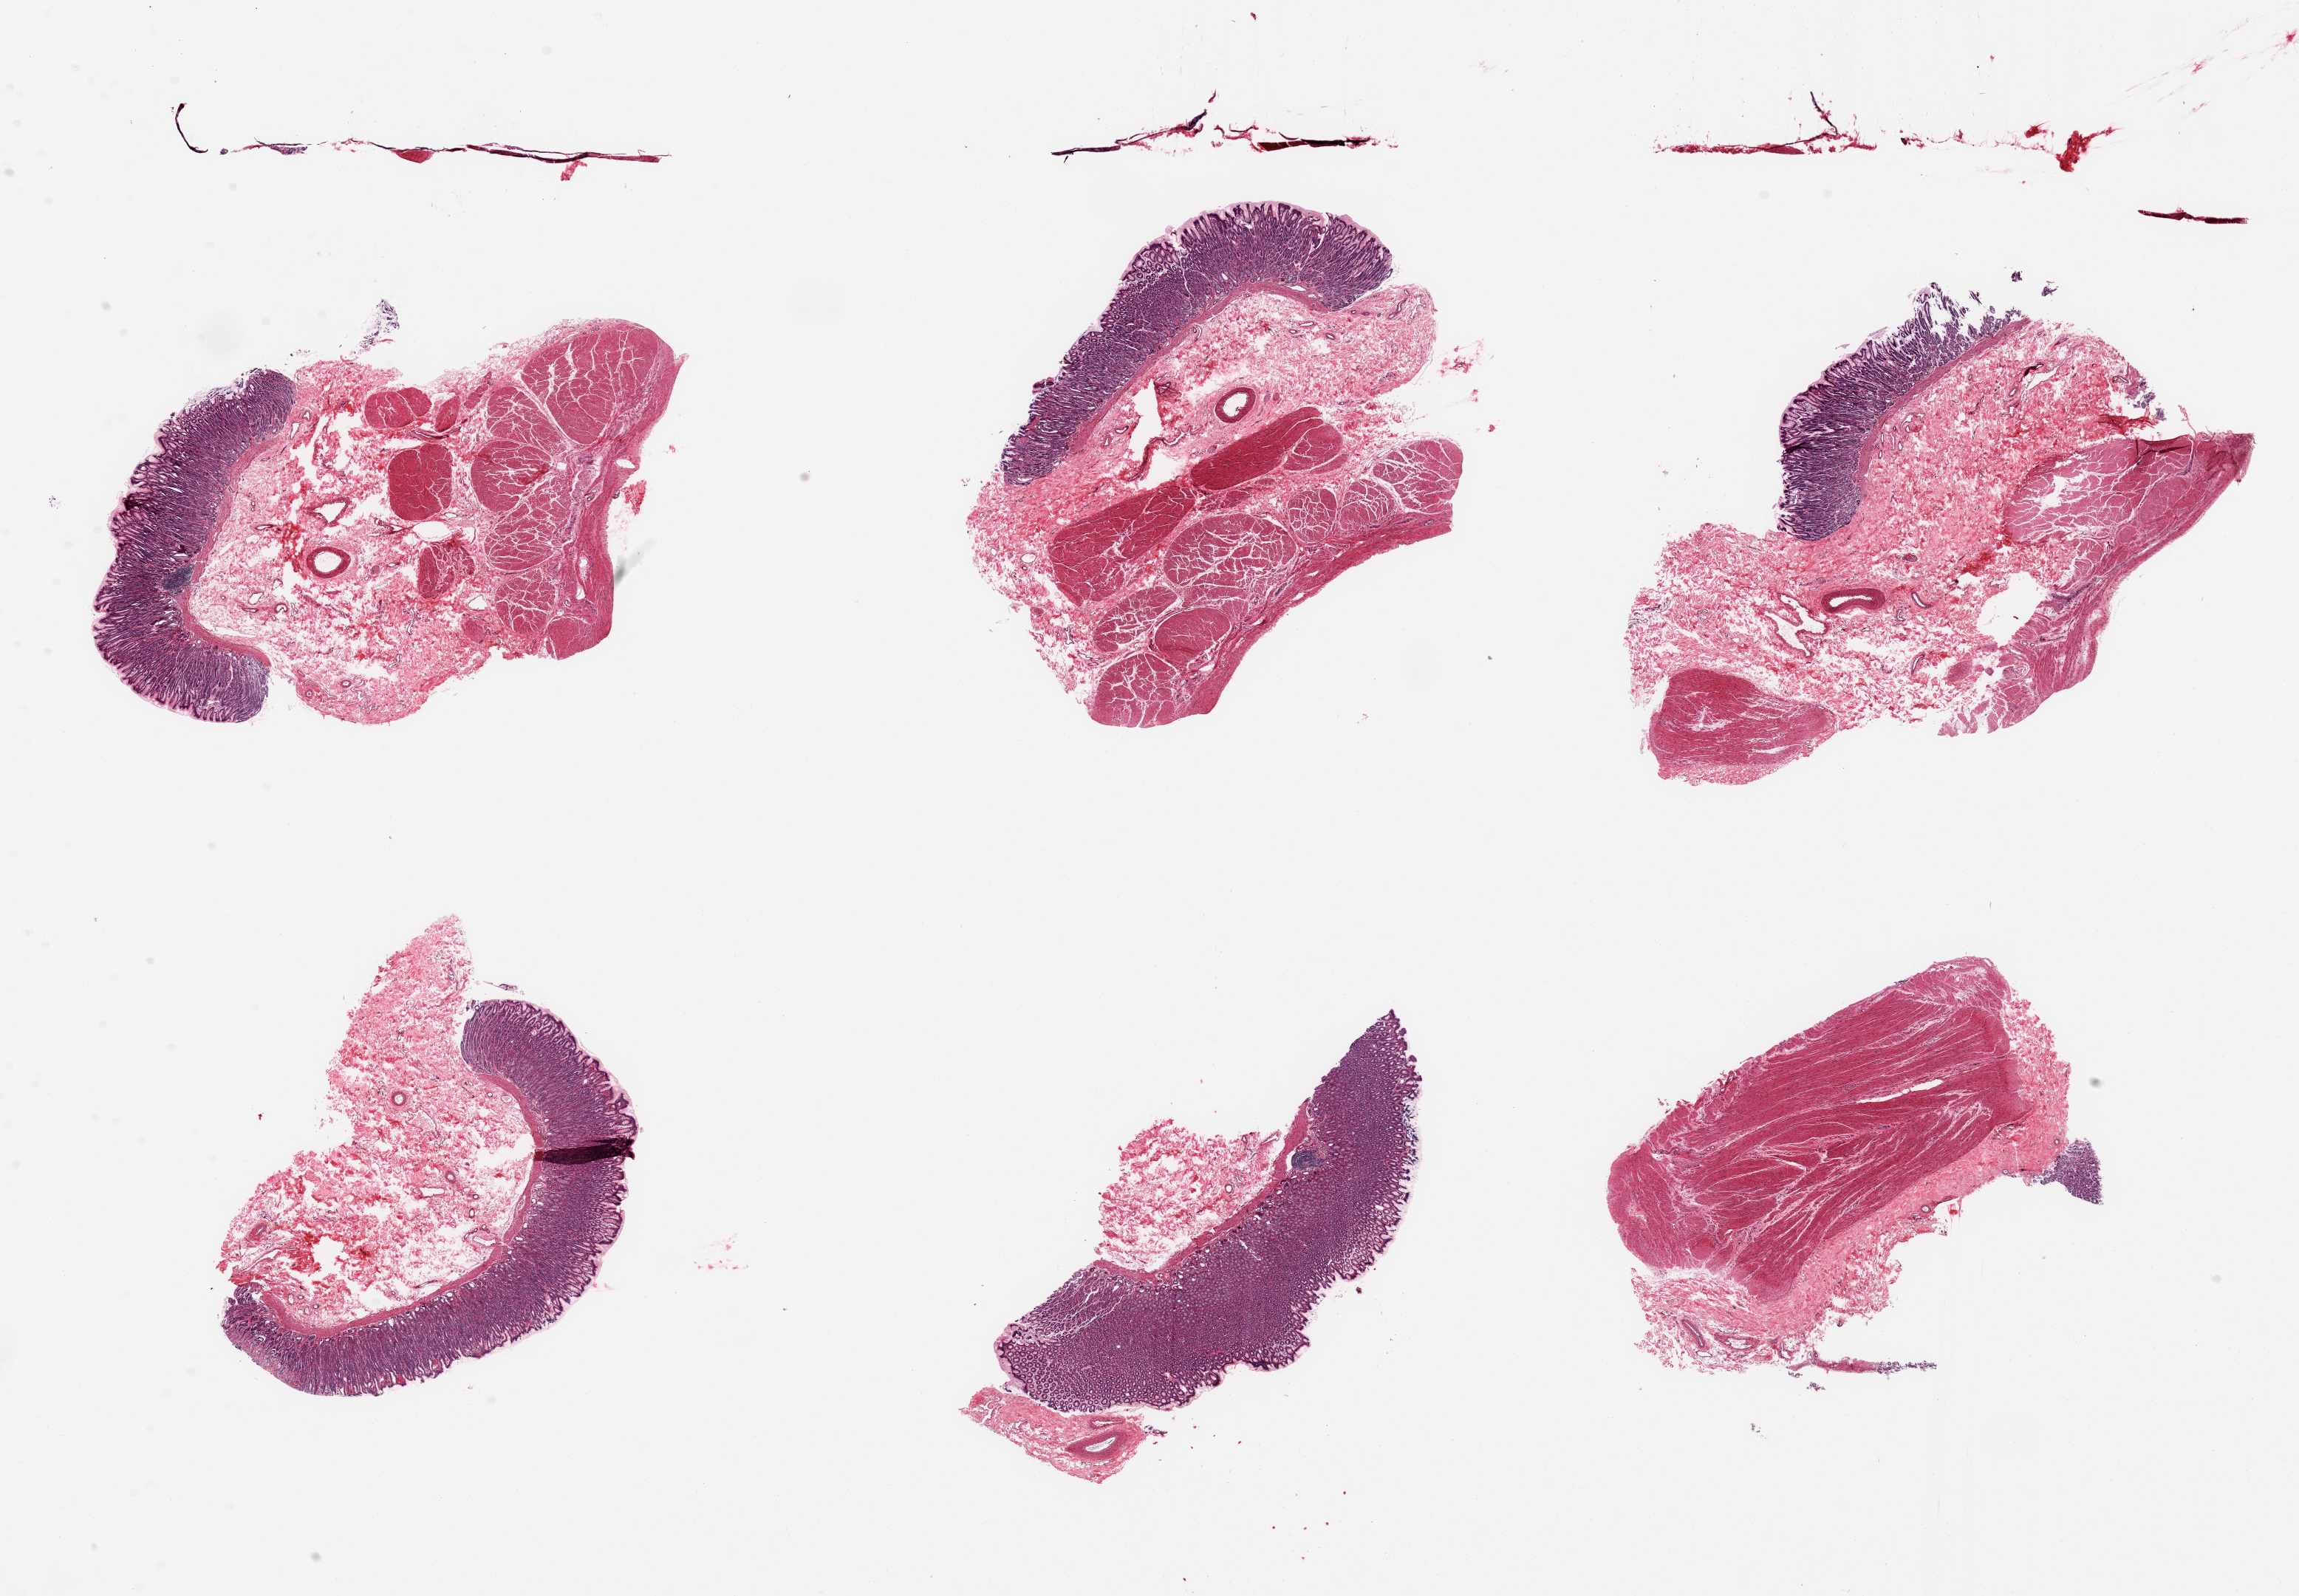
Haematoxylin and eosin whole-slide image, brightfield, whole scanned area (about 24.6 x 17.1 mm) shown as a low-resolution overview; PAXgene-fixed paraffin-embedded (PFPE) section; sampled site (target tissue): stomach; donor tissue sample. Male donor.
- review note (as recorded): 6 pieces, mucosa well- preserved up to ~1mm, ~30% thickness. Deep microglandular dilation or gastropathic changes